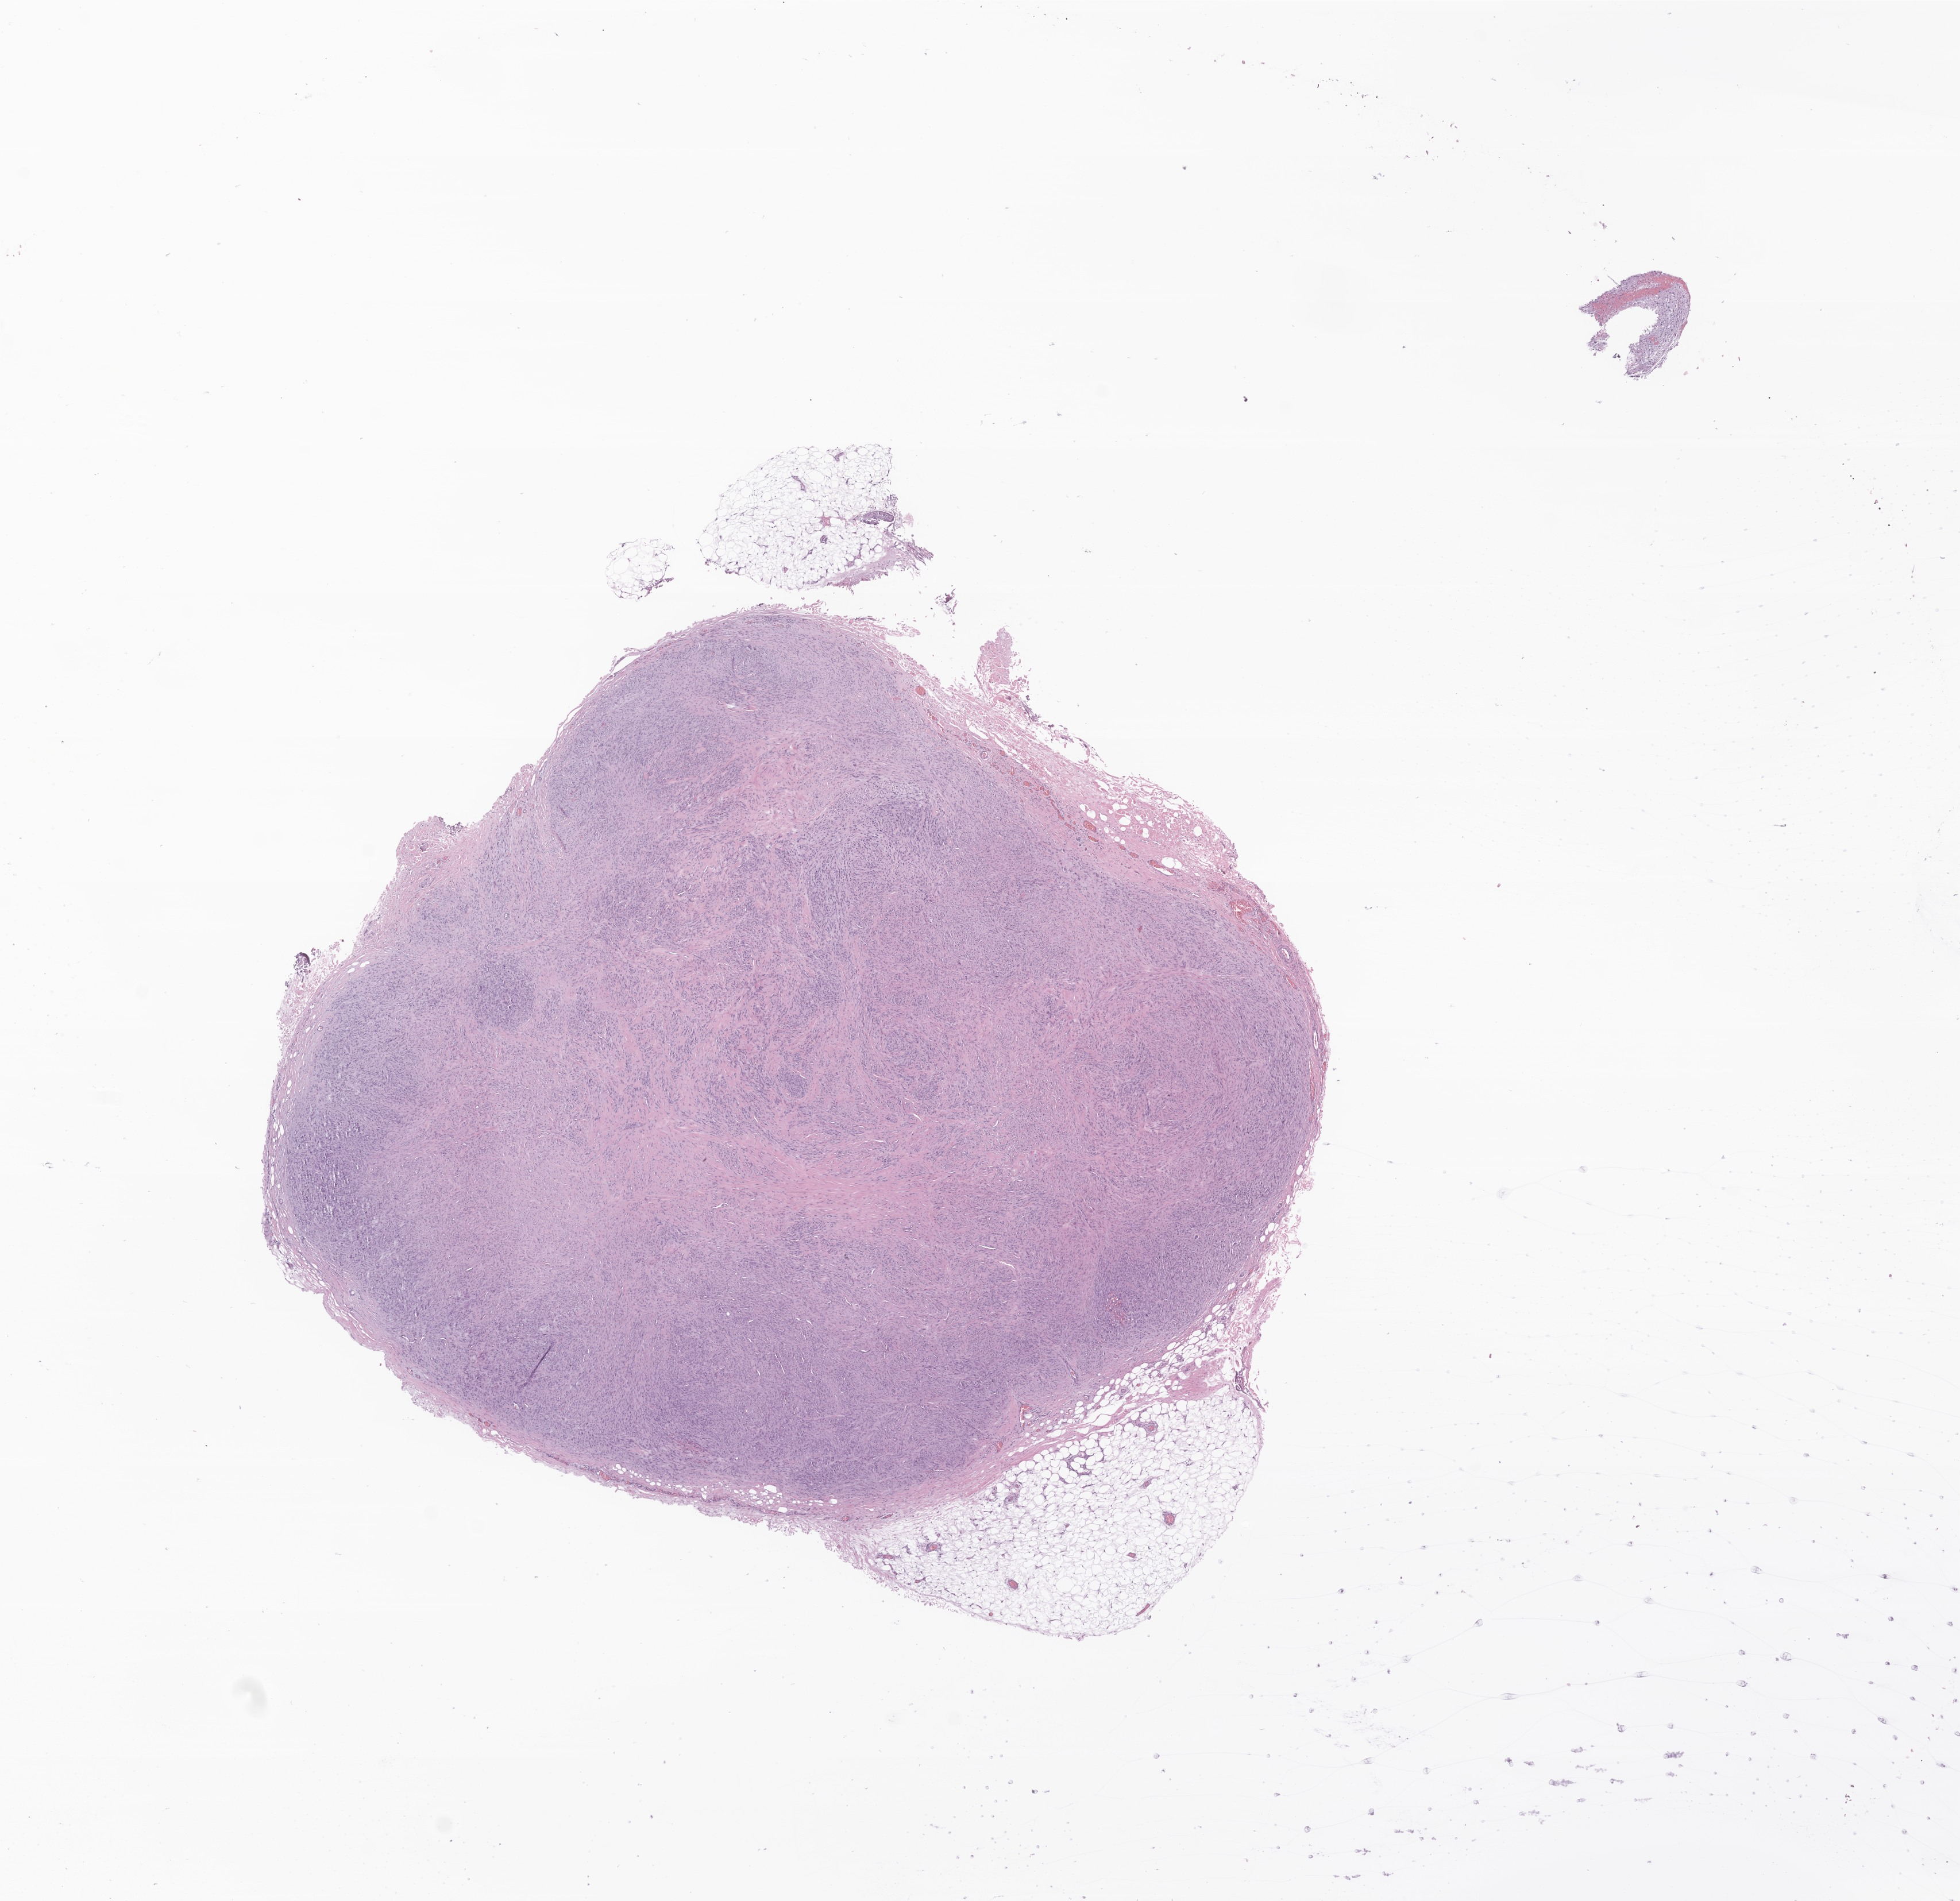
Hematoxylin and eosin (H&E) whole-slide image of tumor tissue from the soft tissue of lower extremity, shown as a low-resolution overview of the whole scanned area (about 14.4 x 14.0 mm), FFPE section. Patient: male, age 184 months (15 years 4 months).
Diagnosis (ICD-O-3 morphology term): Undifferentiated sarcoma. Tissue or organ of origin (case record): connective, subcutaneous and other soft tissues of lower limb and hip.